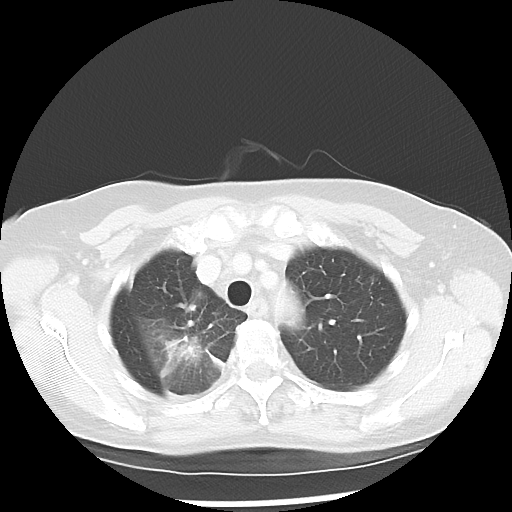
Chest CT, one axial slice; position 41 of 52 along the scan axis; lung window (W 1500 / L -600 HU); 512 × 512 image matrix, field of view 328 × 328 mm. Female patient, age 60 years. Case-level facts recorded for this patient, not image findings: clinical TNM (as recorded): T2 N1 M1a.
Outlined on this slice (rectangle marked by the reading radiologist):
- lung tumour (recorded histology: adenocarcinoma): bounding box (x1, y1, x2, y2) in pixels: (155, 333, 213, 387)